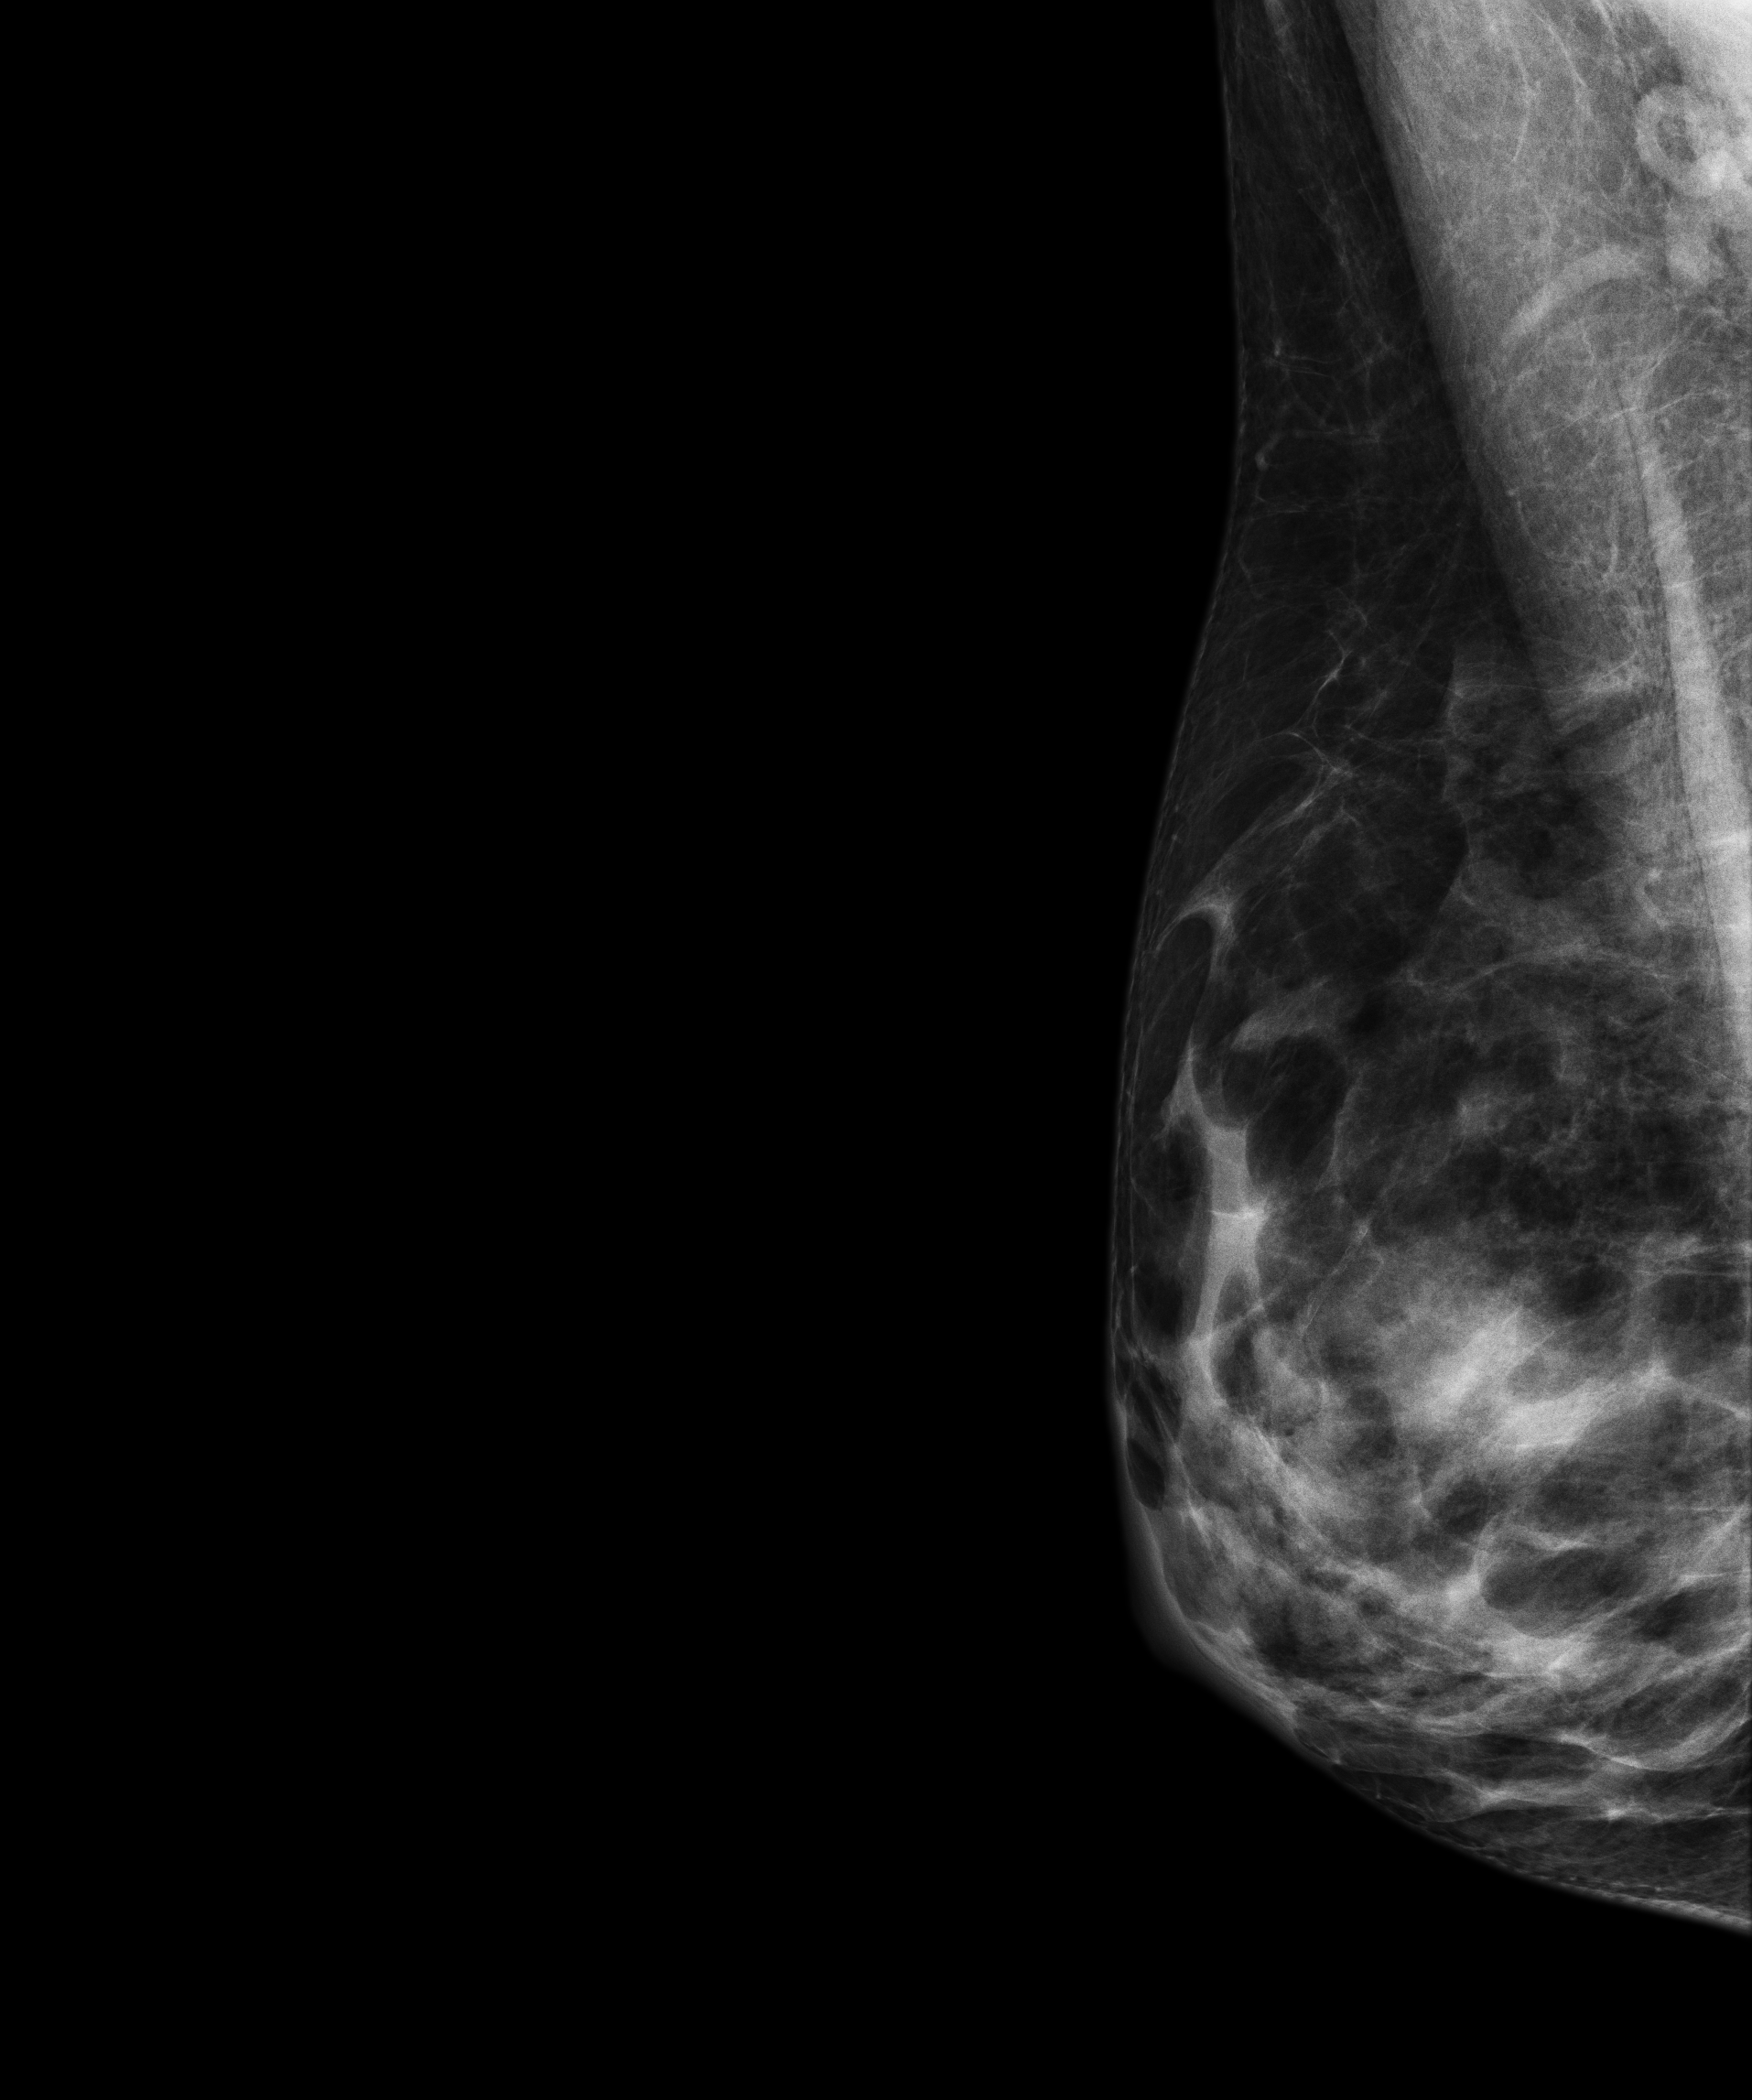
Screening examination; compressed breast thickness 48 mm; system: Senographe Essential ADS_56.21.3. Patient aged 66 years (female).
Image type: full-field digital mammogram. Breast: right. Projection: medio-lateral oblique projection.